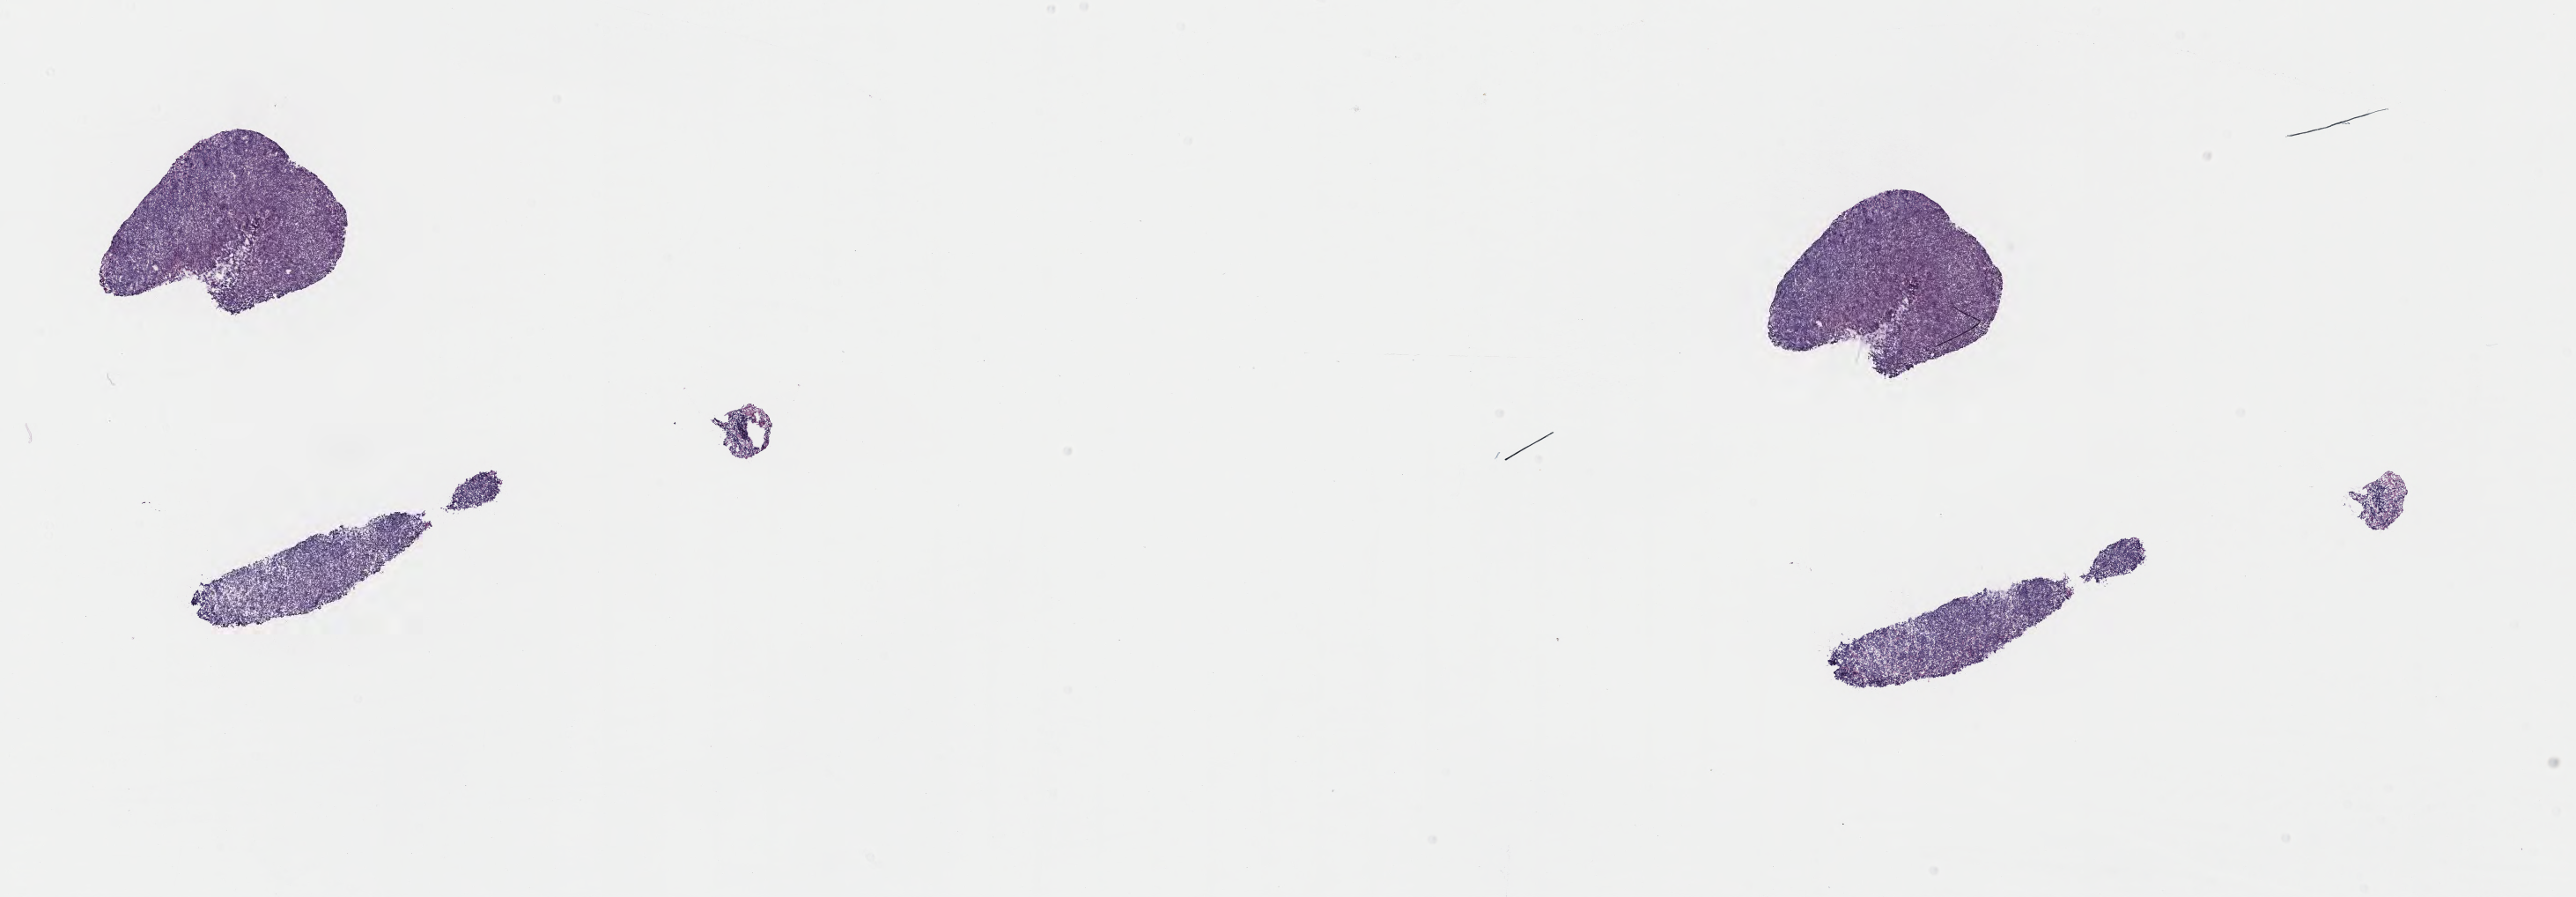
Whole-slide image, hematoxylin and eosin (H&E) stain, whole scanned area (about 23.7 x 8.2 mm) shown as a low-resolution overview; frozen section; primary tumor; site: abdomen proper. Patient: female, age at initial diagnosis 7 years. Slide review estimates, as recorded: tumor cells 95%, tumor nuclei 95%, stromal cells 0%, necrosis 5%, normal cells 0%. Infiltration values recorded for this section: lymphocyte infiltration 40%, monocyte infiltration 35%, neutrophil infiltration 0%.
Diagnosis: Burkitt lymphoma, NOS. Section: top of the tissue portion. Ann Arbor stage (patient): Stage III.